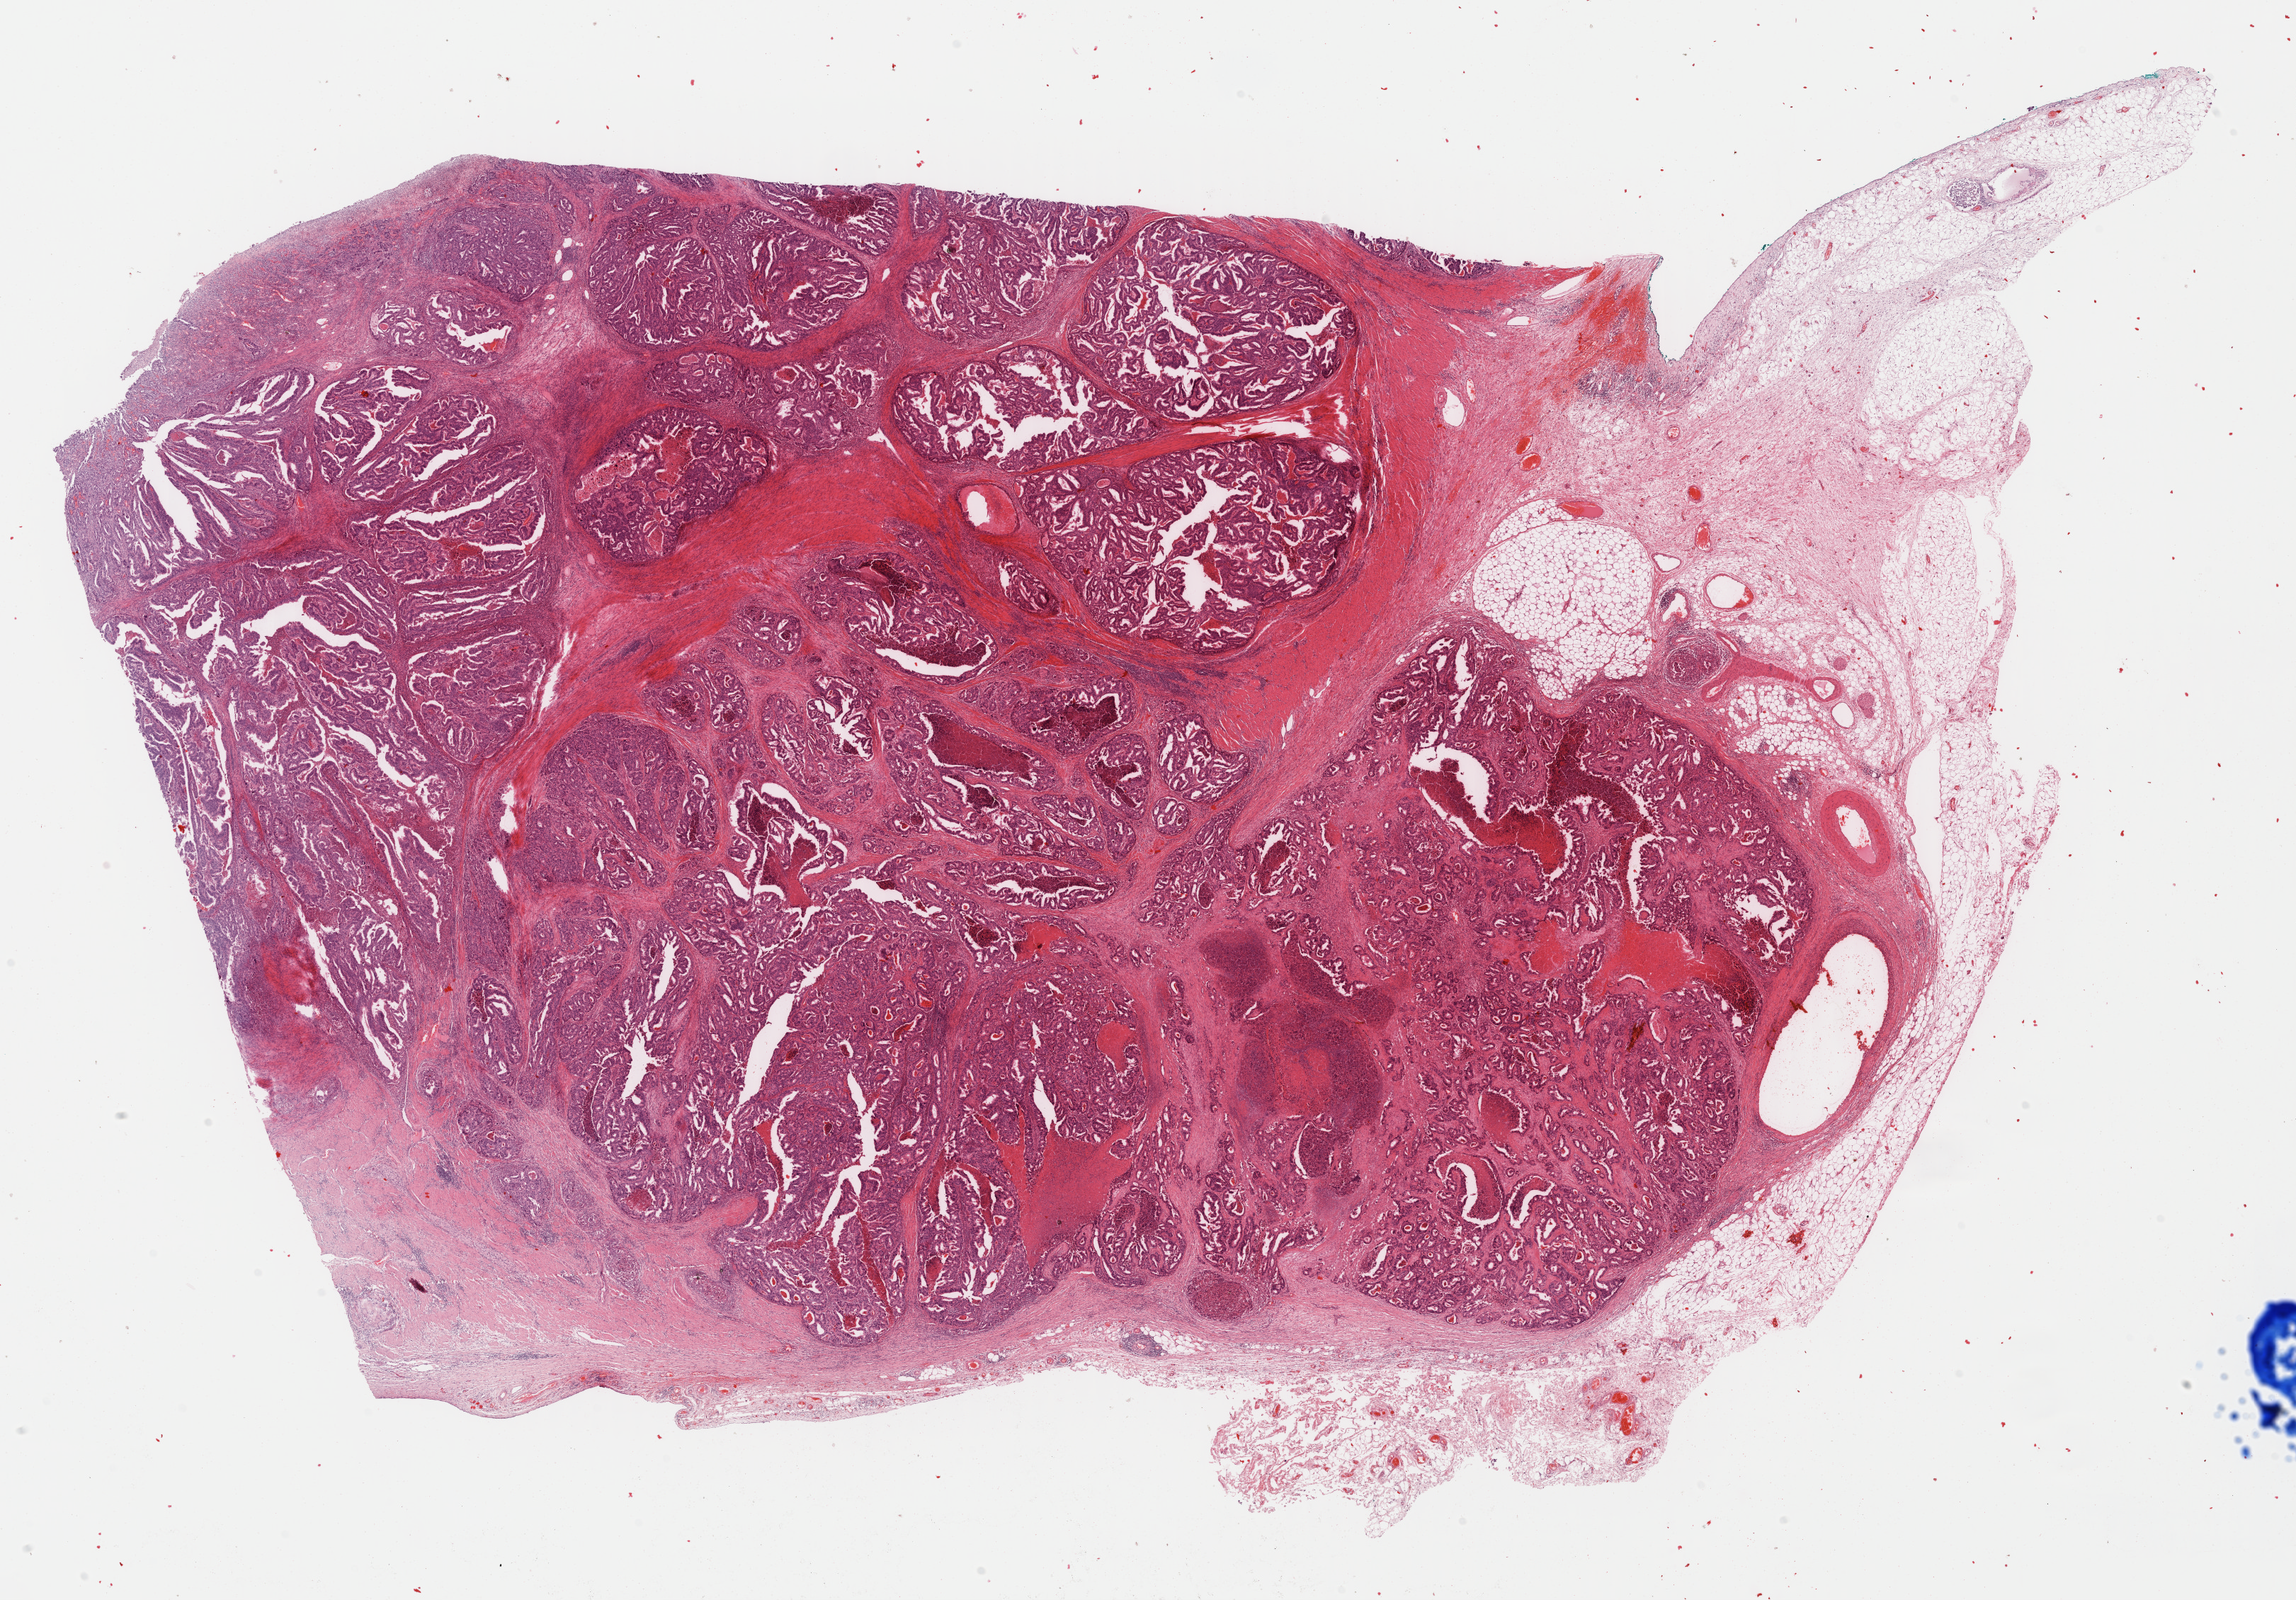
Digitized H&E-stained tissue section (whole slide), low-resolution overview of the scanned area, about 25.5 x 17.8 mm (from a 40x scan). Formalin-fixed paraffin-embedded (FFPE) diagnostic section. Primary tumour sample from the stomach. Male, age 77 years at initial diagnosis. Histologic grade: G2 (moderately differentiated).
AJCC pathologic stage: IB. Lymph nodes positive (case pathology): 0 of 7 examined. Diagnosis: Tubular adenocarcinoma (body of stomach).